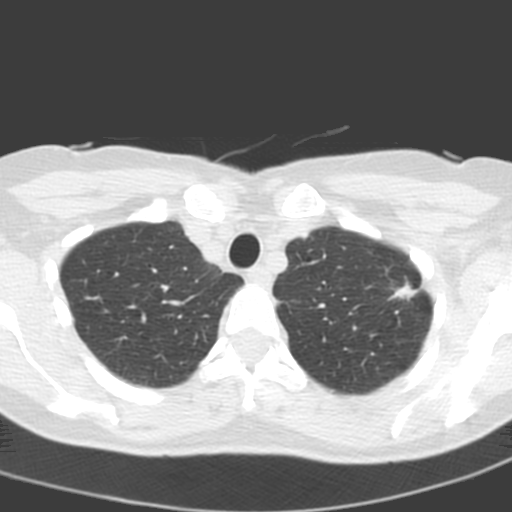
Axial slice from a low-dose chest CT screening exam. First (baseline) screen. Lung window (W 1500 / L -600 HU). 3.2 mm slice thickness. Slice 32 of 193 in the series. 512 × 512 image matrix, field of view 272 × 272 mm. Female participant, aged 58 years at enrolment. Current smoker at enrolment.
• Expert reader's lesion annotation, box from (x=380, y=270) to (x=426, y=317) px.
• The exam's reader record, not a measurement of the box and not confirmed to be the same lesion: non-calcified nodule or mass ≥4 mm, left upper lobe, 14 × 10 mm, spiculated (stellate) margins, soft tissue attenuation.
• Official screen result: positive, change unspecified: nodule(s) >= 4 mm or enlarging nodule(s), mass(es), or other non-specific abnormalities suspicious for lung cancer.
• Lung cancer was diagnosed 48 days after this screen: adenocarcinoma, NOS, left upper lobe, poorly differentiated (G3), stage IA (AJCC 6th edition), 13 mm at pathology.